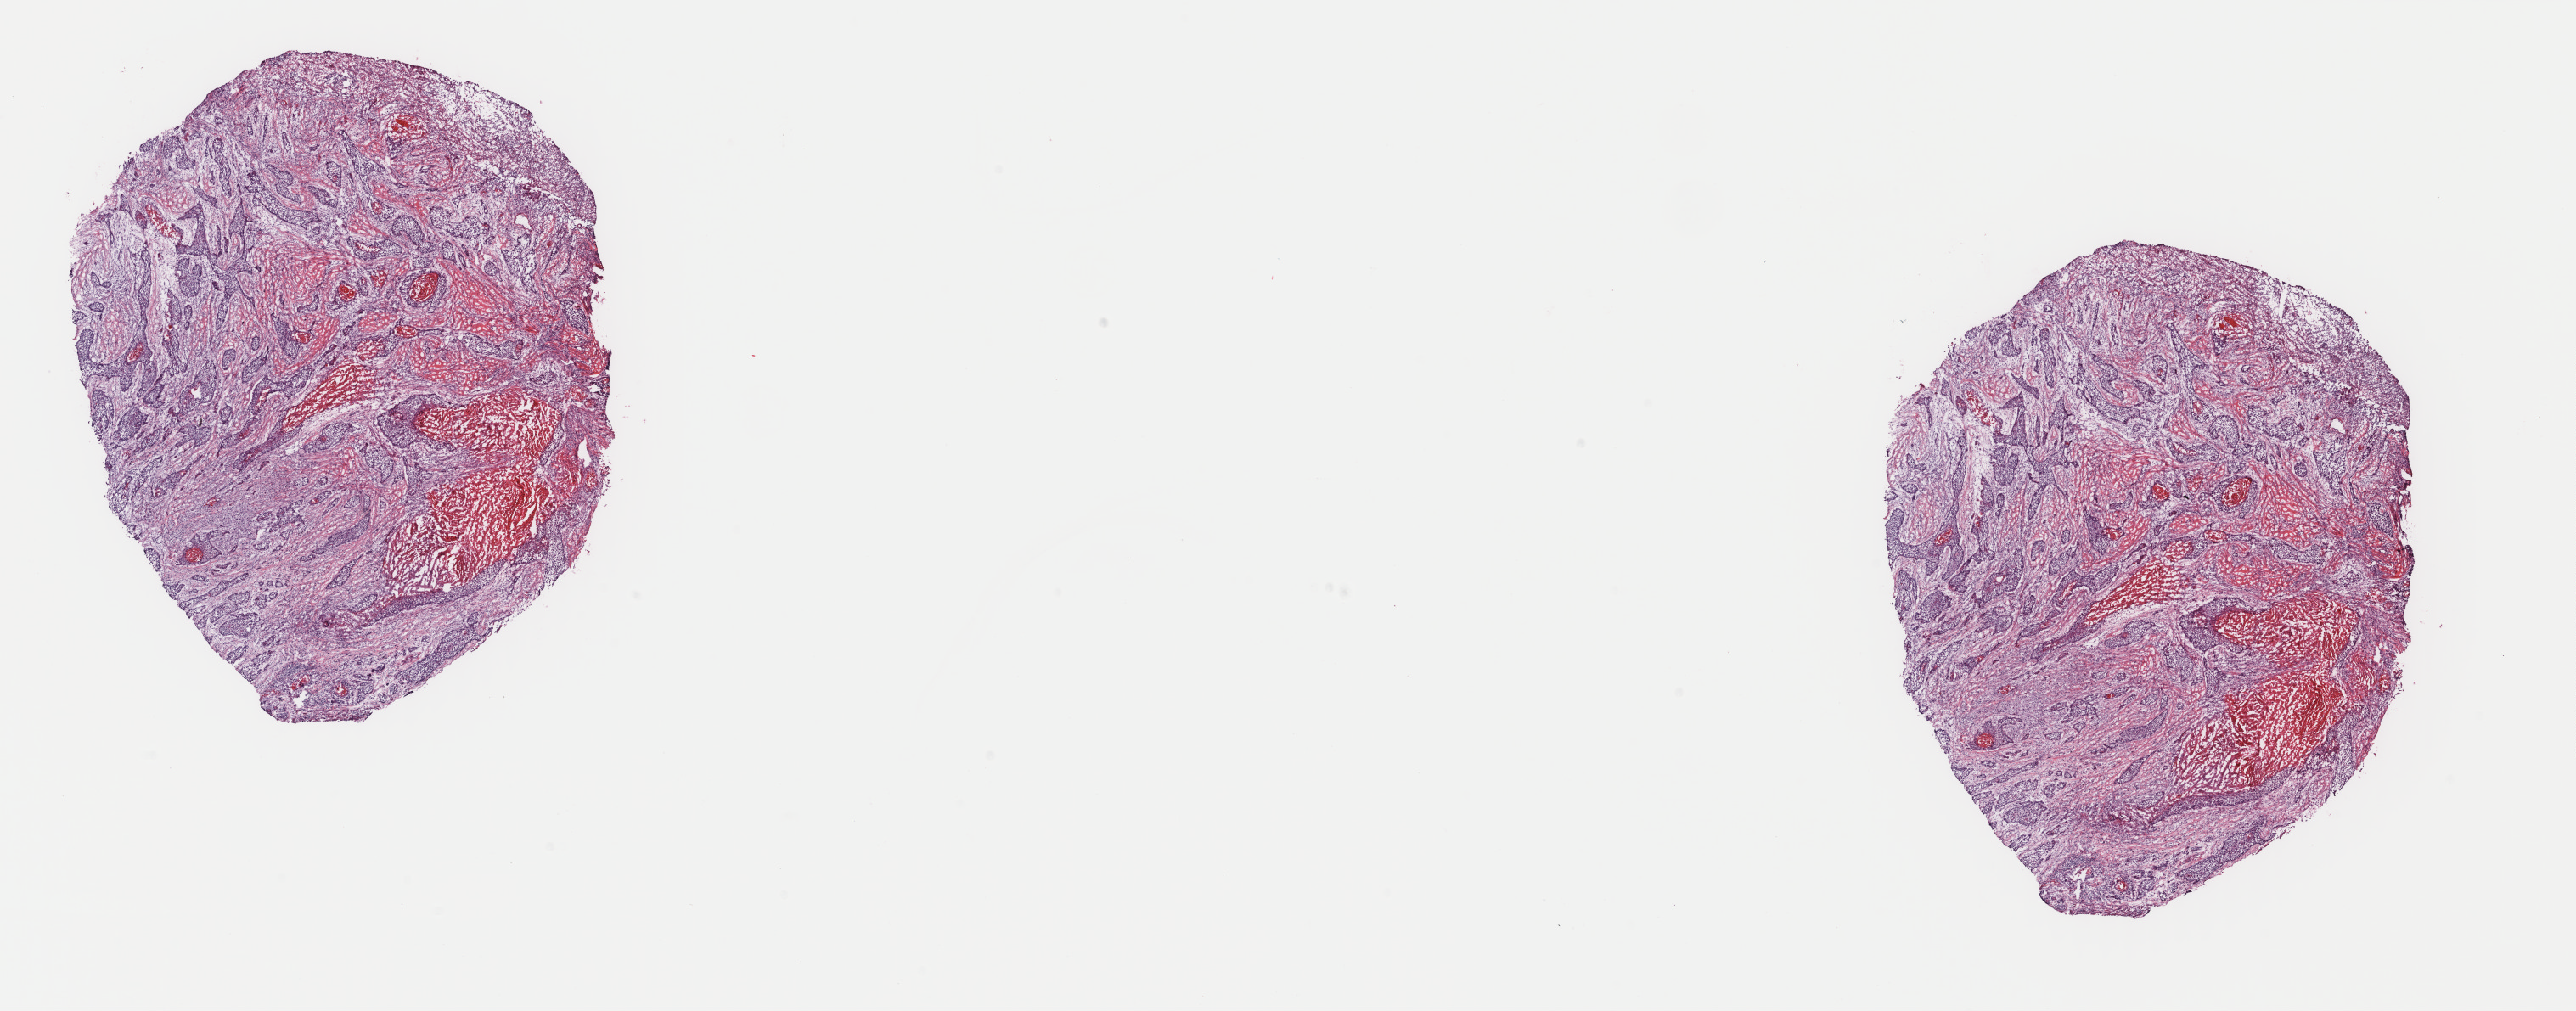
Whole-slide histology image, Hematoxylin and eosin (H&E) stained, whole scanned area (about 24.1 x 9.5 mm) shown as a low-resolution overview. Frozen section from the top of the tissue portion. Head and neck, primary tumour sample. Male, age 75 years at initial diagnosis. Histologic grade: G2 (moderately differentiated). Pathologist review of this section (percent, as recorded): tumour cells 50%, tumour nuclei 70%, normal cells 0%, stromal cells 50%, necrosis 0%. Infiltration values recorded for this section: lymphocyte infiltration 10%, monocyte infiltration 0%, neutrophil infiltration 0%.
Diagnosis: Squamous cell carcinoma, NOS (larynx, NOS). Lymph nodes positive (case pathology): 0 of 18 examined. AJCC pathologic stage: IVA.